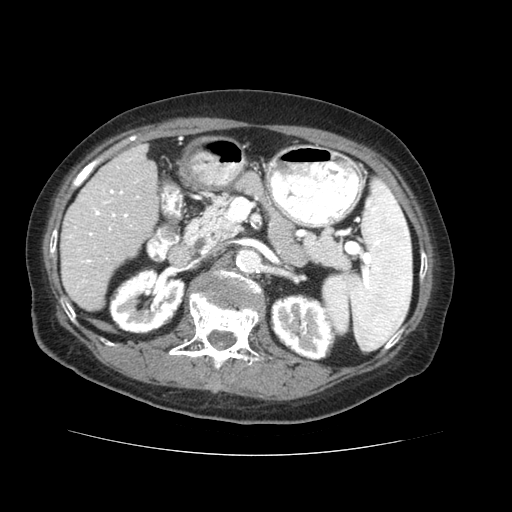
Contrast-enhanced abdominal CT (liver protocol), one axial slice; slice 20 of 73 in the series (ordered by position); soft-tissue window (W 400 / L 40 HU); 2.5 mm slice thickness; 512 × 512 image matrix. From the clinical record (not read from this slice): diagnosis: hepatocellular carcinoma (patient treated with transarterial chemoembolisation; whether this scan precedes or follows treatment is not stated here); TNM stage (as recorded): Stage-IVB; Child-Pugh class: A.
Annotated regions visible in this slice (semi-automatic segmentation, software-assisted and operator-edited):
- liver parenchyma outside the tumour (the mass and vessels are separate outlines, so this box may not span the whole liver): bounding box (x1, y1, x2, y2) in pixels: (60, 144, 158, 310)
- liver vessels: (67, 158, 140, 287)